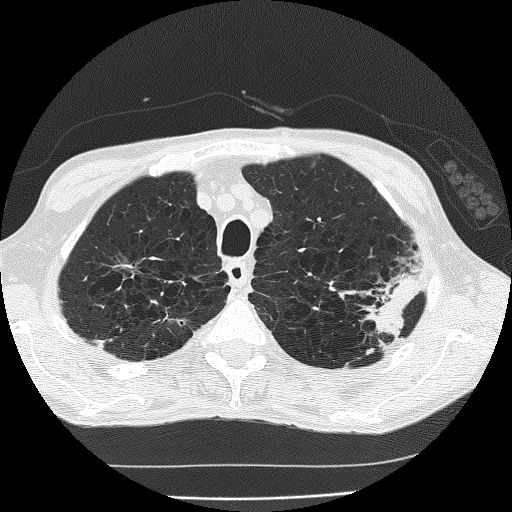
Low-dose screening chest CT, one axial slice; position 150 of 185 along the scan axis; reconstruction kernel FC51; 120 kVp; lung window (W 1500 / L -600 HU); 2 mm slice thickness; 512 × 512 image matrix, field of view 320 × 320 mm.
Annotated regions visible in this slice (expert manual segmentation):
- lesion 1 (tumor, upper lobe of left lung): bounding box [x1, y1, x2, y2] px = [366, 273, 422, 336]